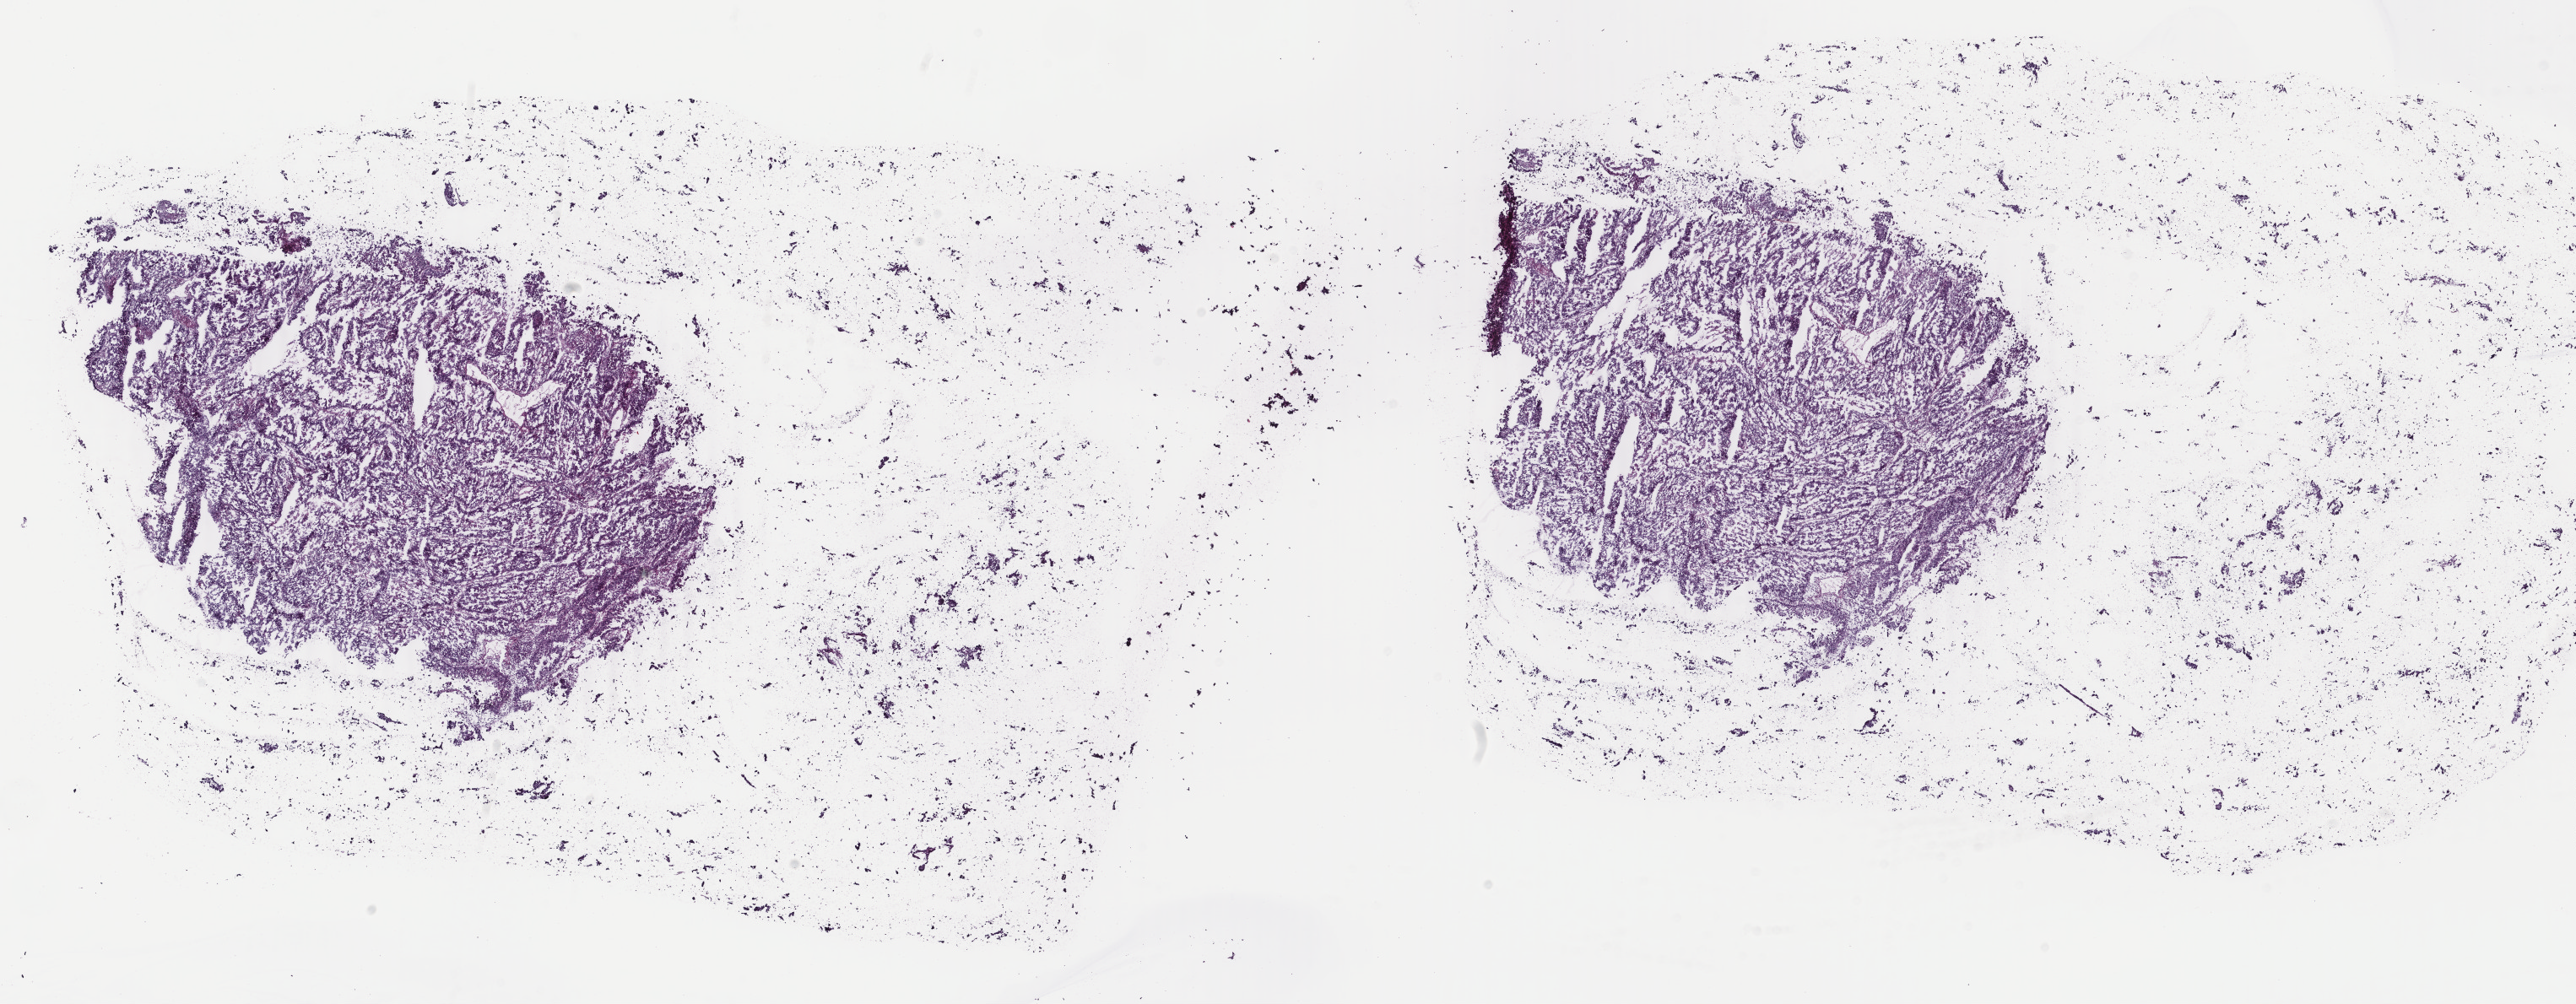
Digitized Hematoxylin and eosin (H&E) stained tissue section (whole slide) — whole scanned area (about 24.3 x 9.5 mm) shown as a low-resolution overview, frozen section from the top of the tissue portion, sample: primary tumour, uterus. Female, age 65 years at initial diagnosis. Histologic grade: G3 (poorly differentiated). Slide review estimates, as recorded: tumour cells 50%, tumour nuclei 70%, normal cells 0%, stromal cells 30%, necrosis 20%. Infiltration values recorded for this section: lymphocyte infiltration 10%, monocyte infiltration 0%, neutrophil infiltration 10%.
FIGO stage: IIIC2. Diagnosis: Serous cystadenocarcinoma, NOS (endometrium). Lymph nodes positive (case pathology): 4 of 4 examined.